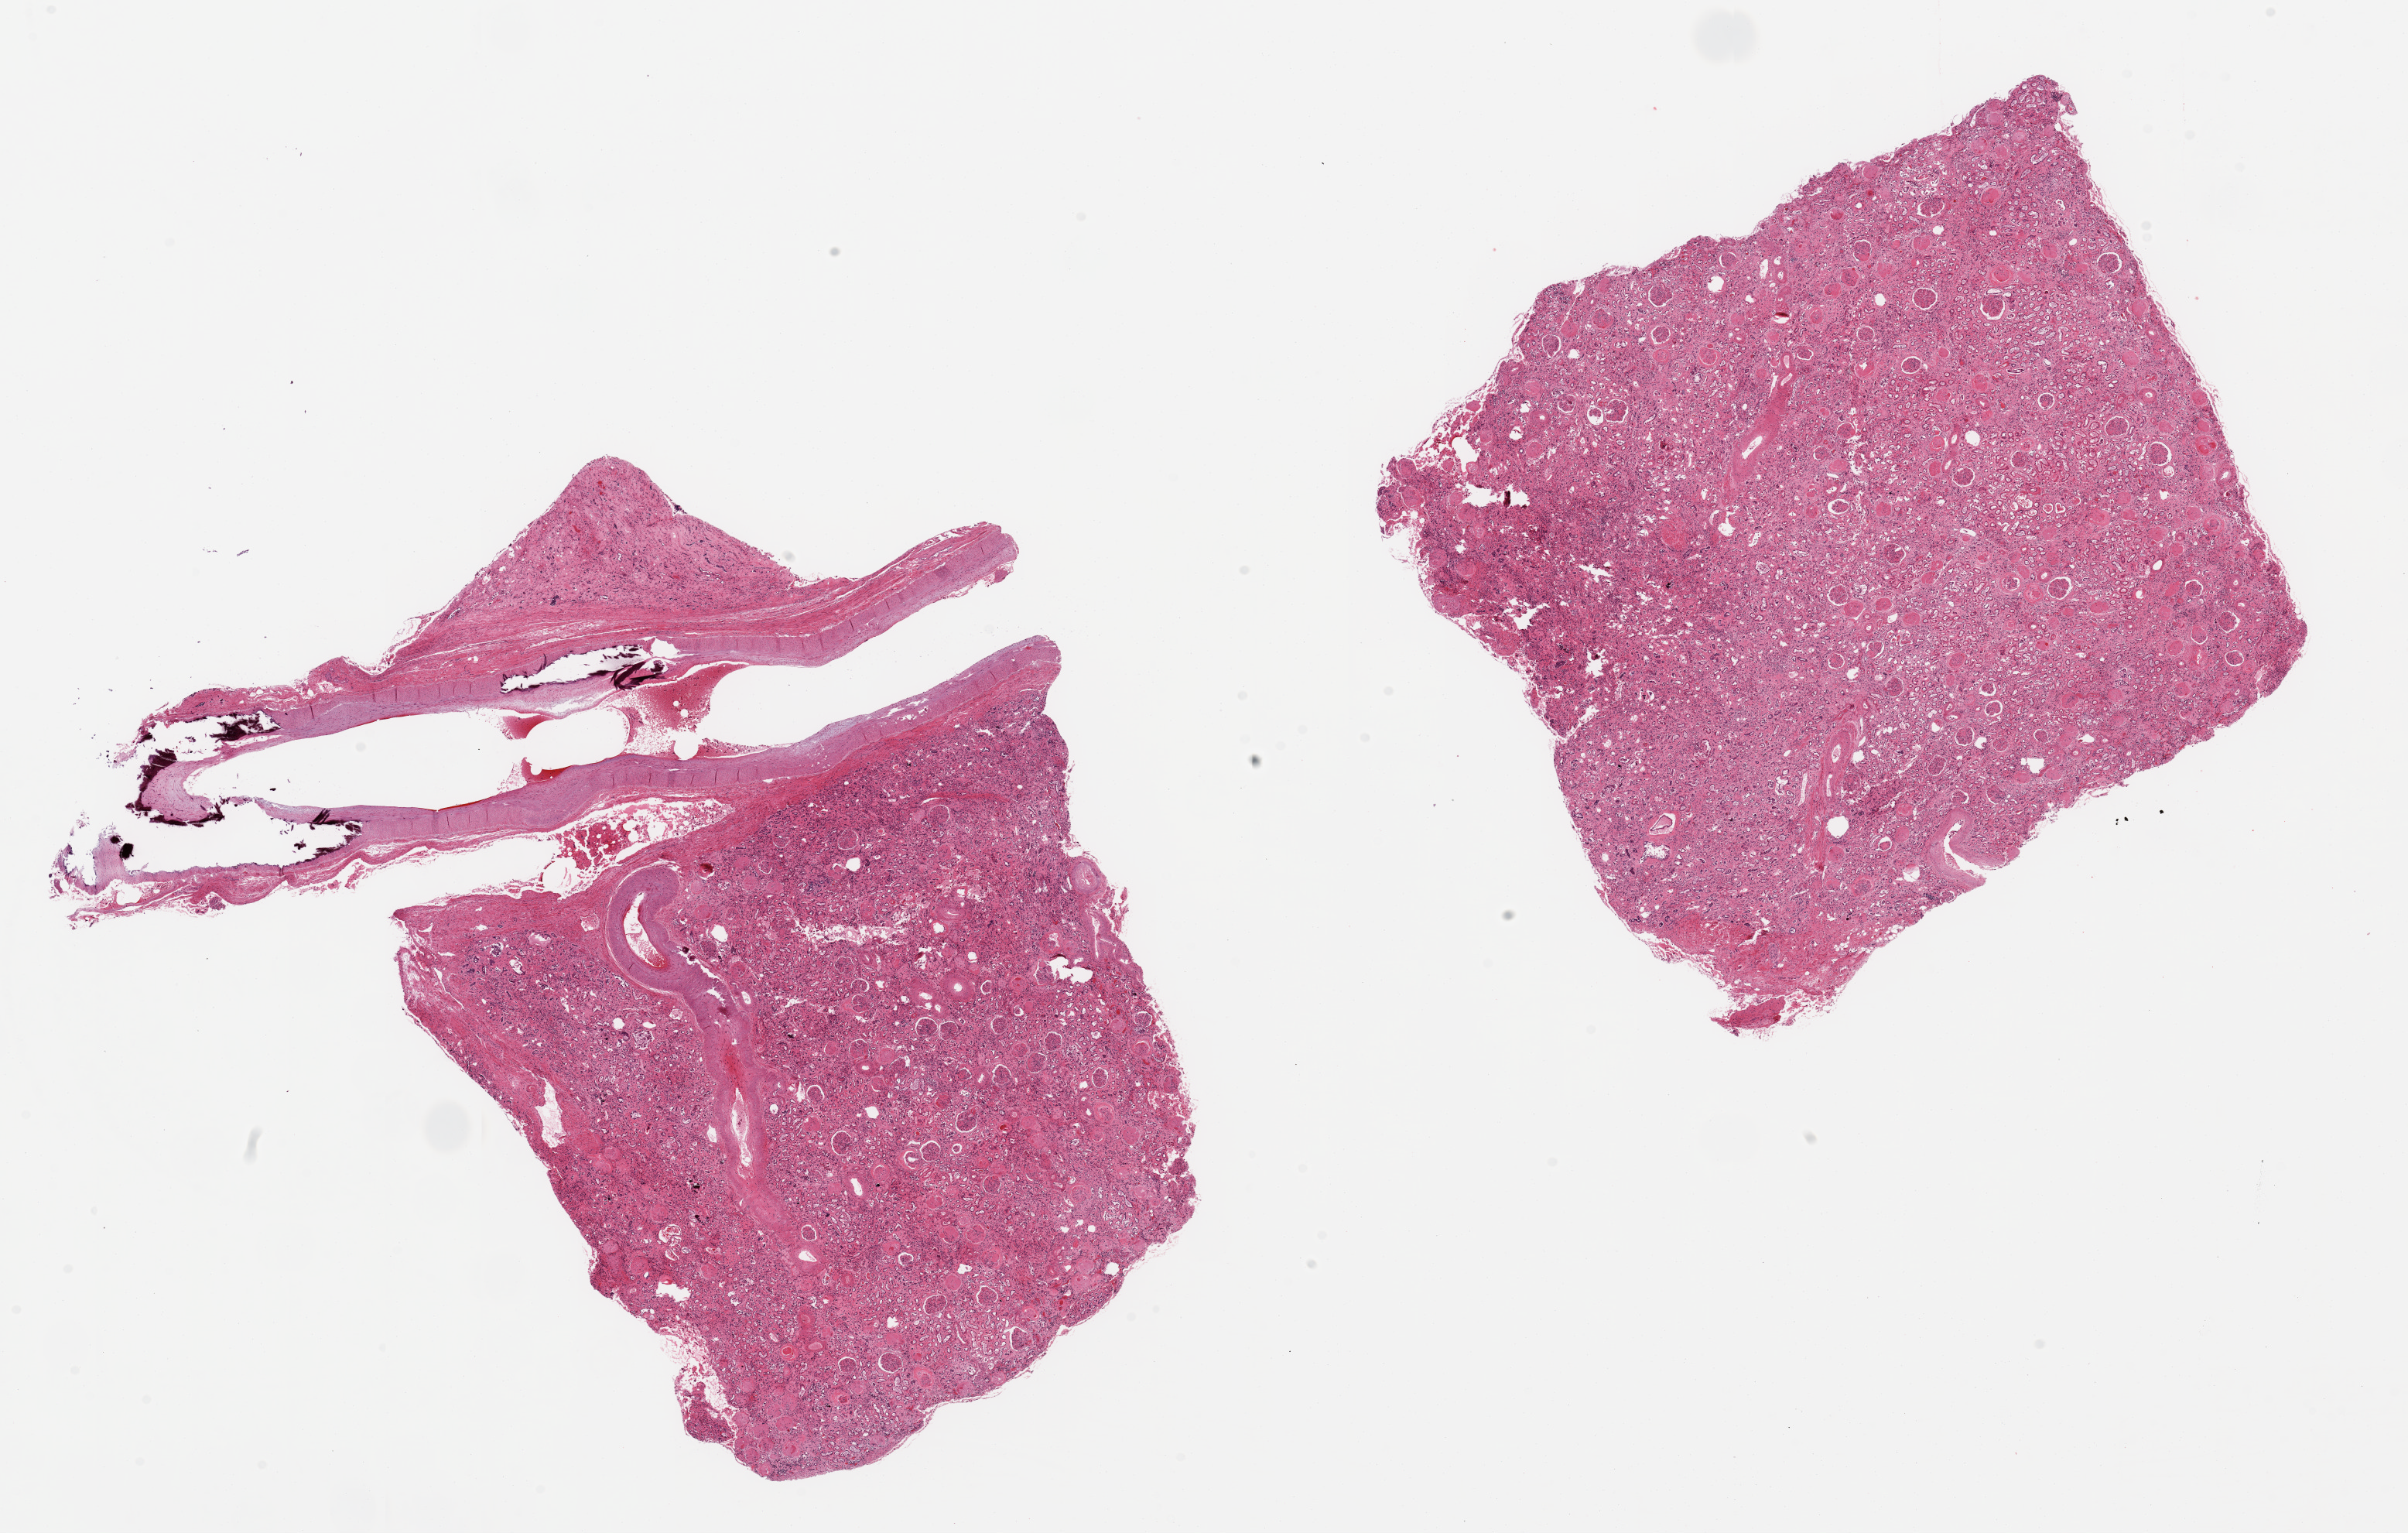
Whole-slide image, hematoxylin and eosin (H&E) stain, brightfield — a low-resolution overview of the entire scanned area, about 24.6 x 15.7 mm; PAXgene-fixed, paraffin-embedded tissue; target tissue: renal medulla; tissue donor sample. Donor sex: female.
• review note (as recorded): 2 ~ 7.5x7mm aliquots, both with glomeruli, must be re-classified as renal cortex, also large fragment (10x2mm) of artery in one aliquot with Mockeberg???s sclerosis